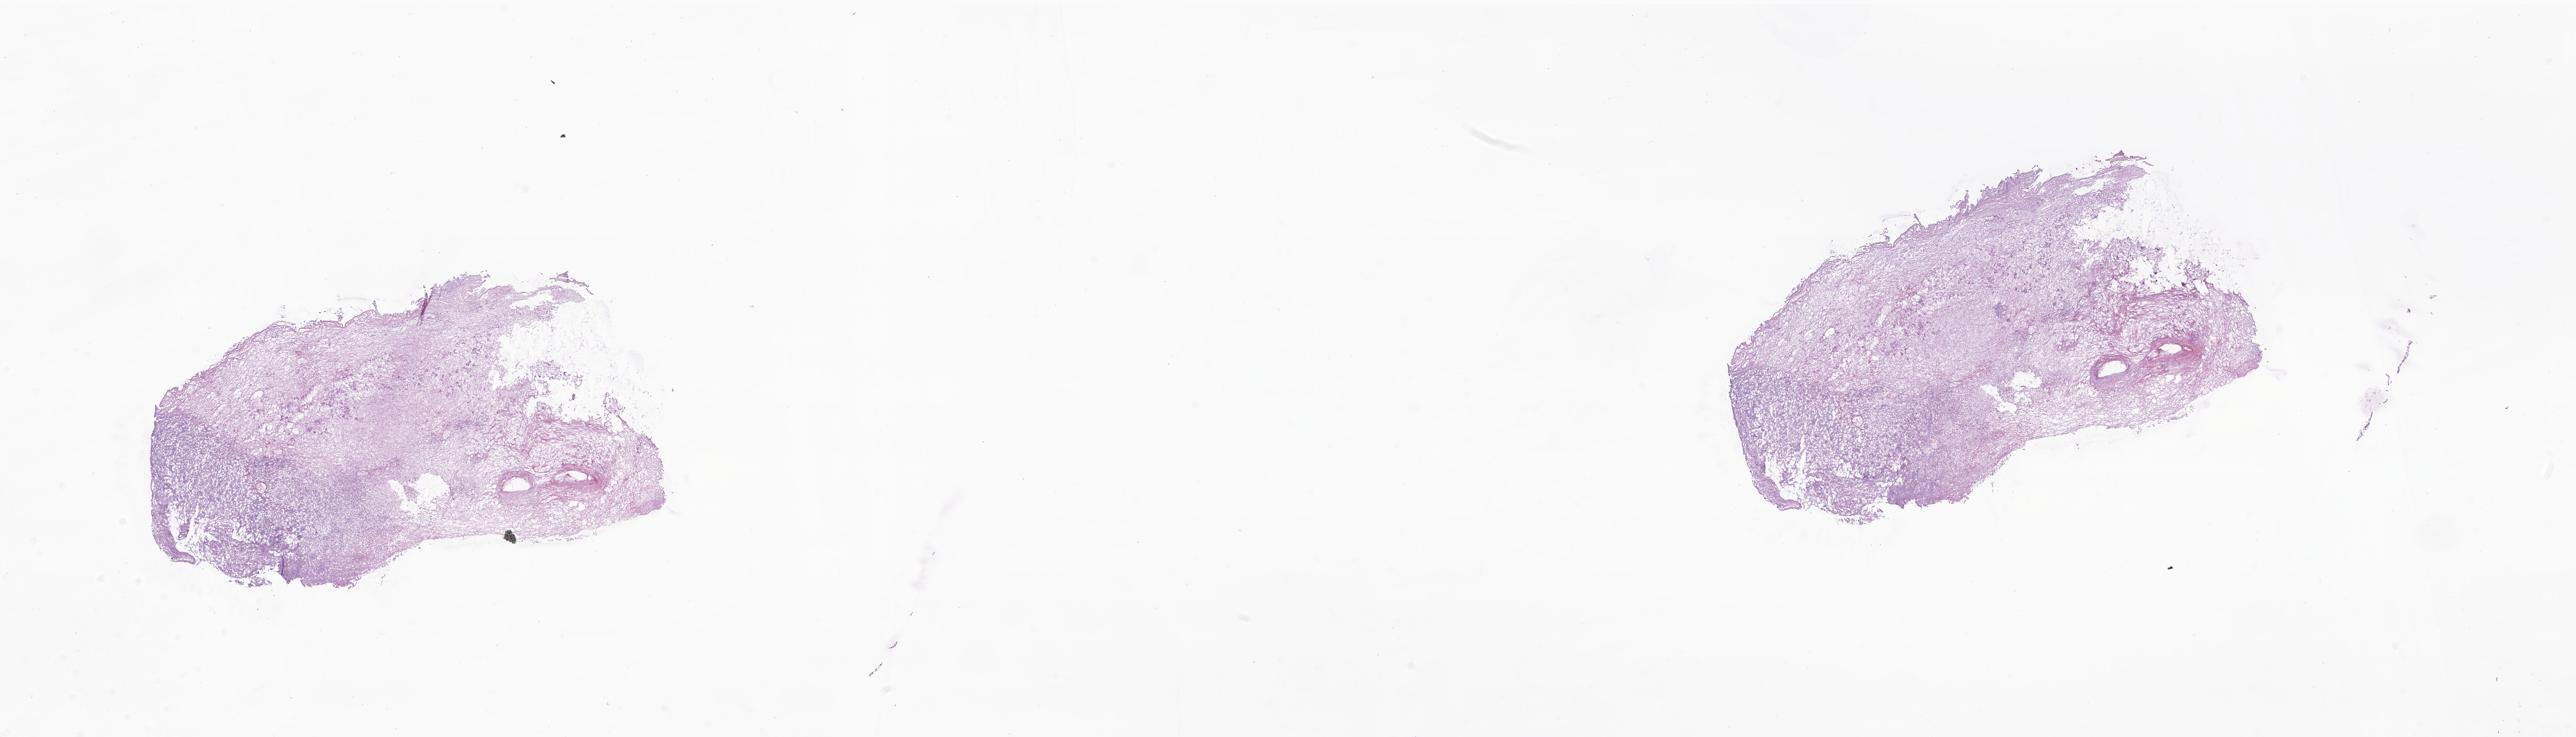
Hematoxylin and eosin (H&E) whole-slide image of tumor tissue from the endocervix — low-resolution overview of the scanned area, about 32.6 x 9.3 mm; frozen section (OCT-embedded). Patient: female, age 227 months (18 years 11 months).
Diagnosis: Embryonal rhabdomyosarcoma, NOS.